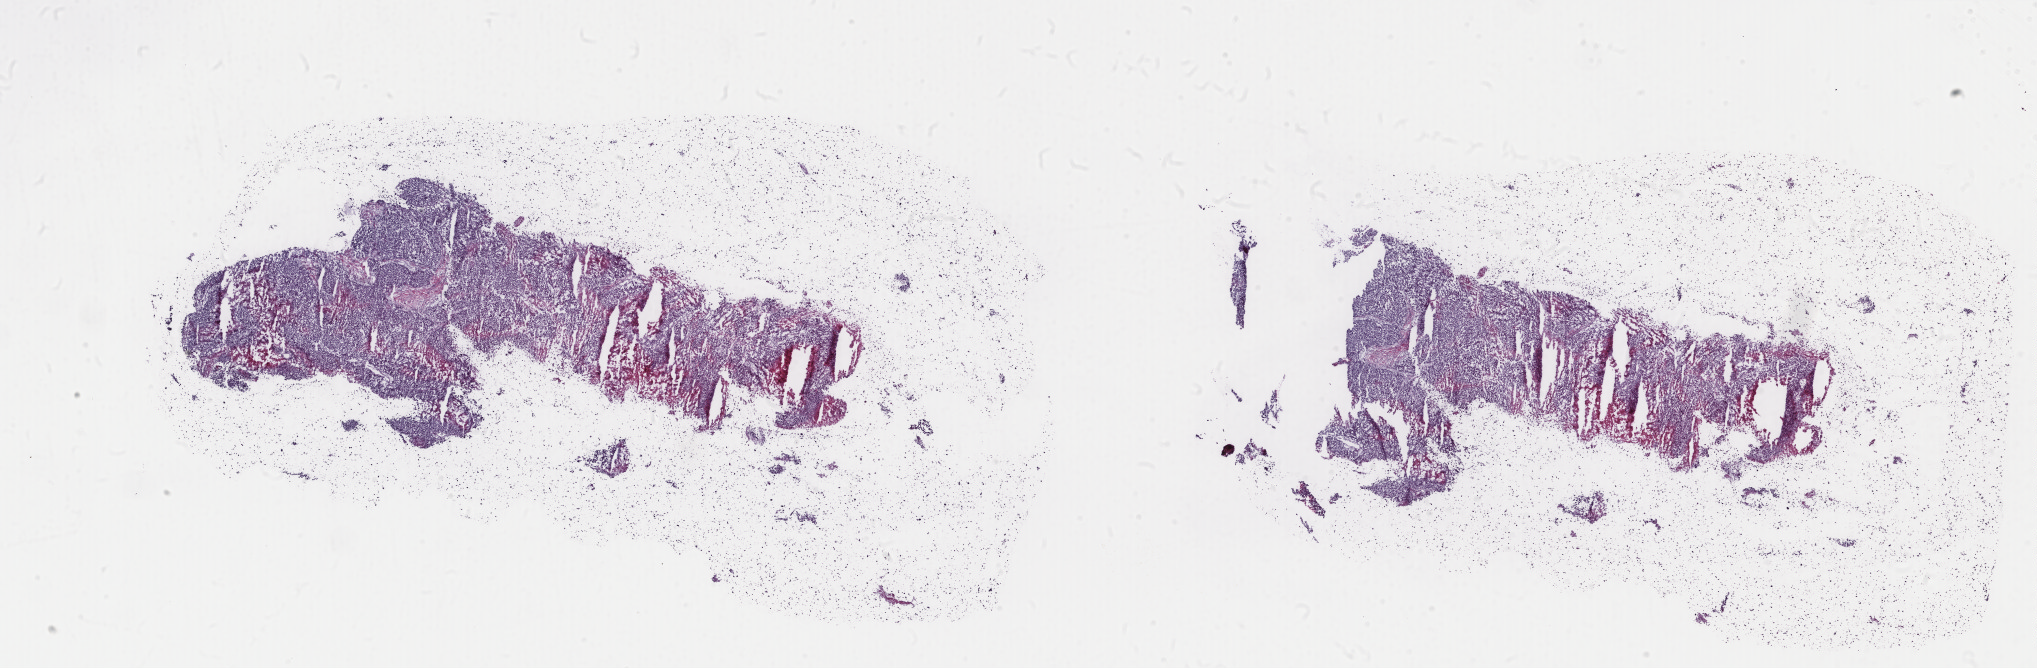
Hematoxylin and eosin (H&E) stained whole-slide image, whole scanned area (about 32.3 x 10.6 mm) shown as a low-resolution overview; frozen section; metastatic tumour sample, sampled site not recorded. Male, age 42 years at initial diagnosis. Slide review estimates, as recorded: tumour cells 80%, tumour nuclei 90%, normal cells 0%, stromal cells 0%, necrosis 20%. Infiltration values recorded for this section: lymphocyte infiltration 0%, monocyte infiltration 0%, neutrophil infiltration 0%.
- this section: metastatic tumour tissue
- patient diagnosis: Malignant melanoma, NOS